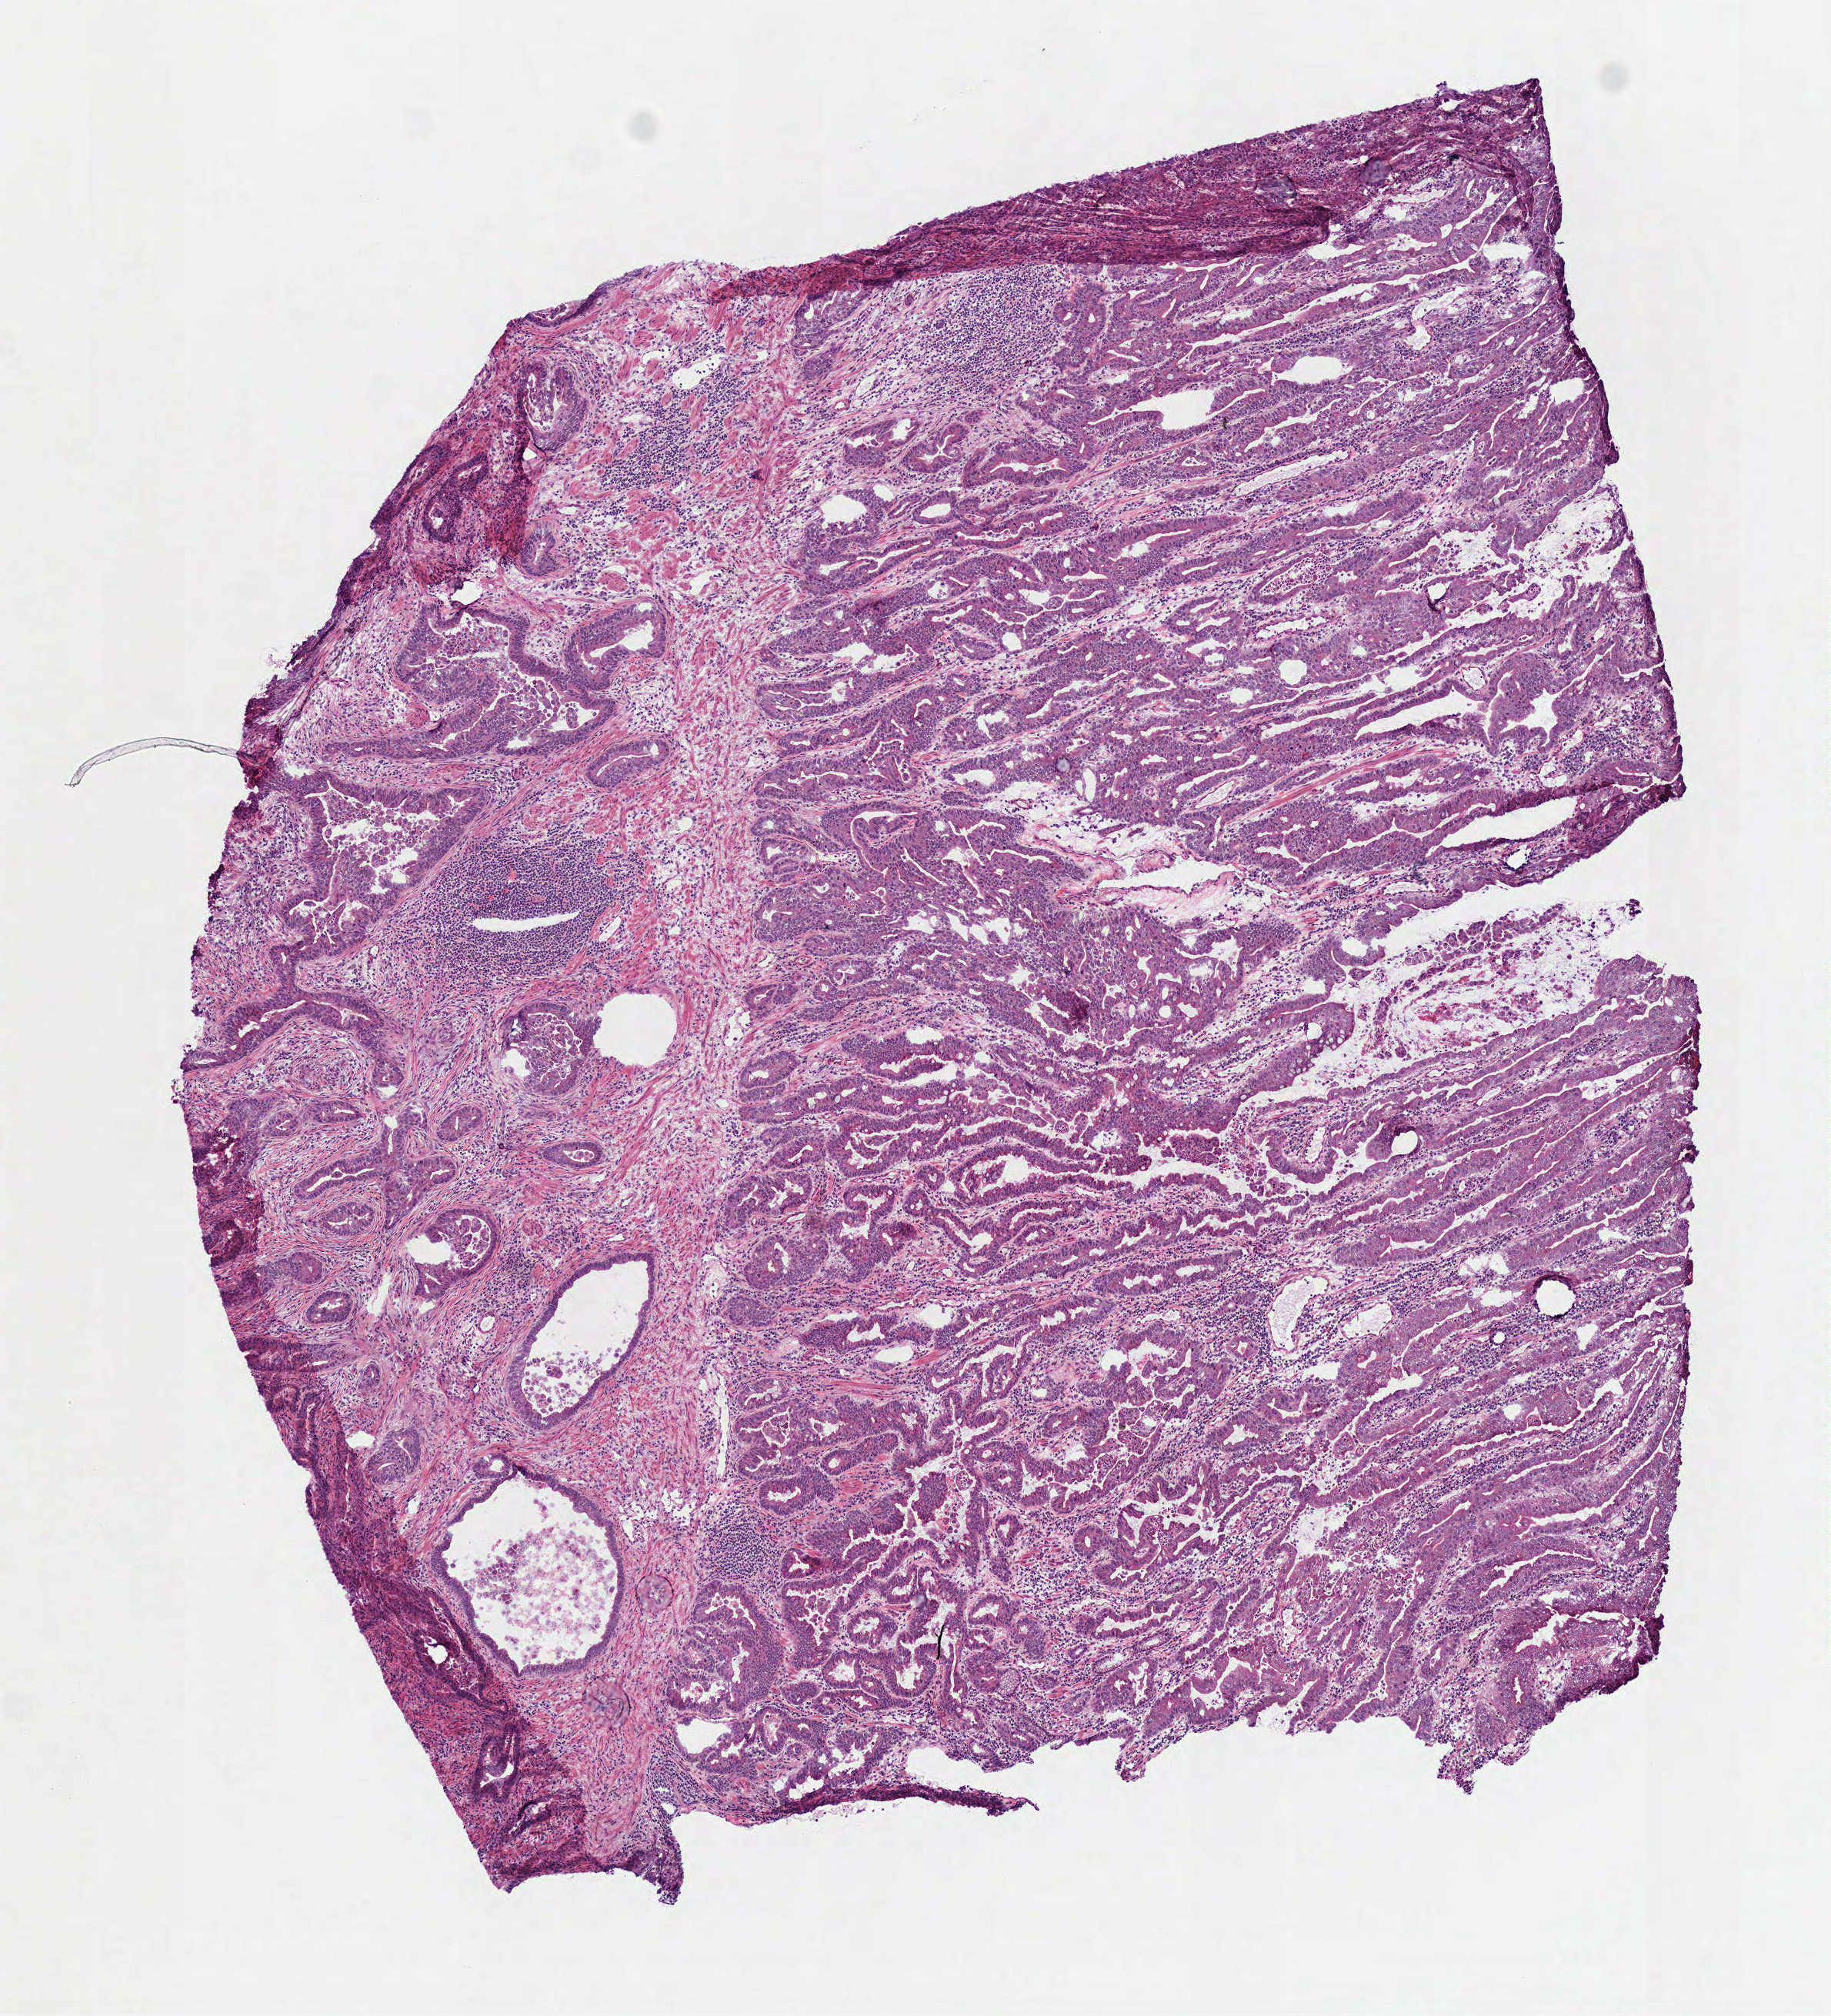
Digitized Hematoxylin and eosin (H&E) stained tissue section (whole slide) — a low-resolution overview of the entire scanned area, about 4.7 x 5.2 mm (slide scanned at 40x); frozen section; sample: primary tumour, stomach. Male, age 63 years at initial diagnosis. Histologic grade: G3 (poorly differentiated). Slide review estimates, as recorded: tumour cells 82%, tumour nuclei 70%, normal cells 0%, stromal cells 18%, necrosis 0%.
* AJCC pathologic stage: IIIA (7th edition)
* histologic diagnosis: Tubular adenocarcinoma (body of stomach)
* lymph nodes positive (case pathology): 20 of 31 examined